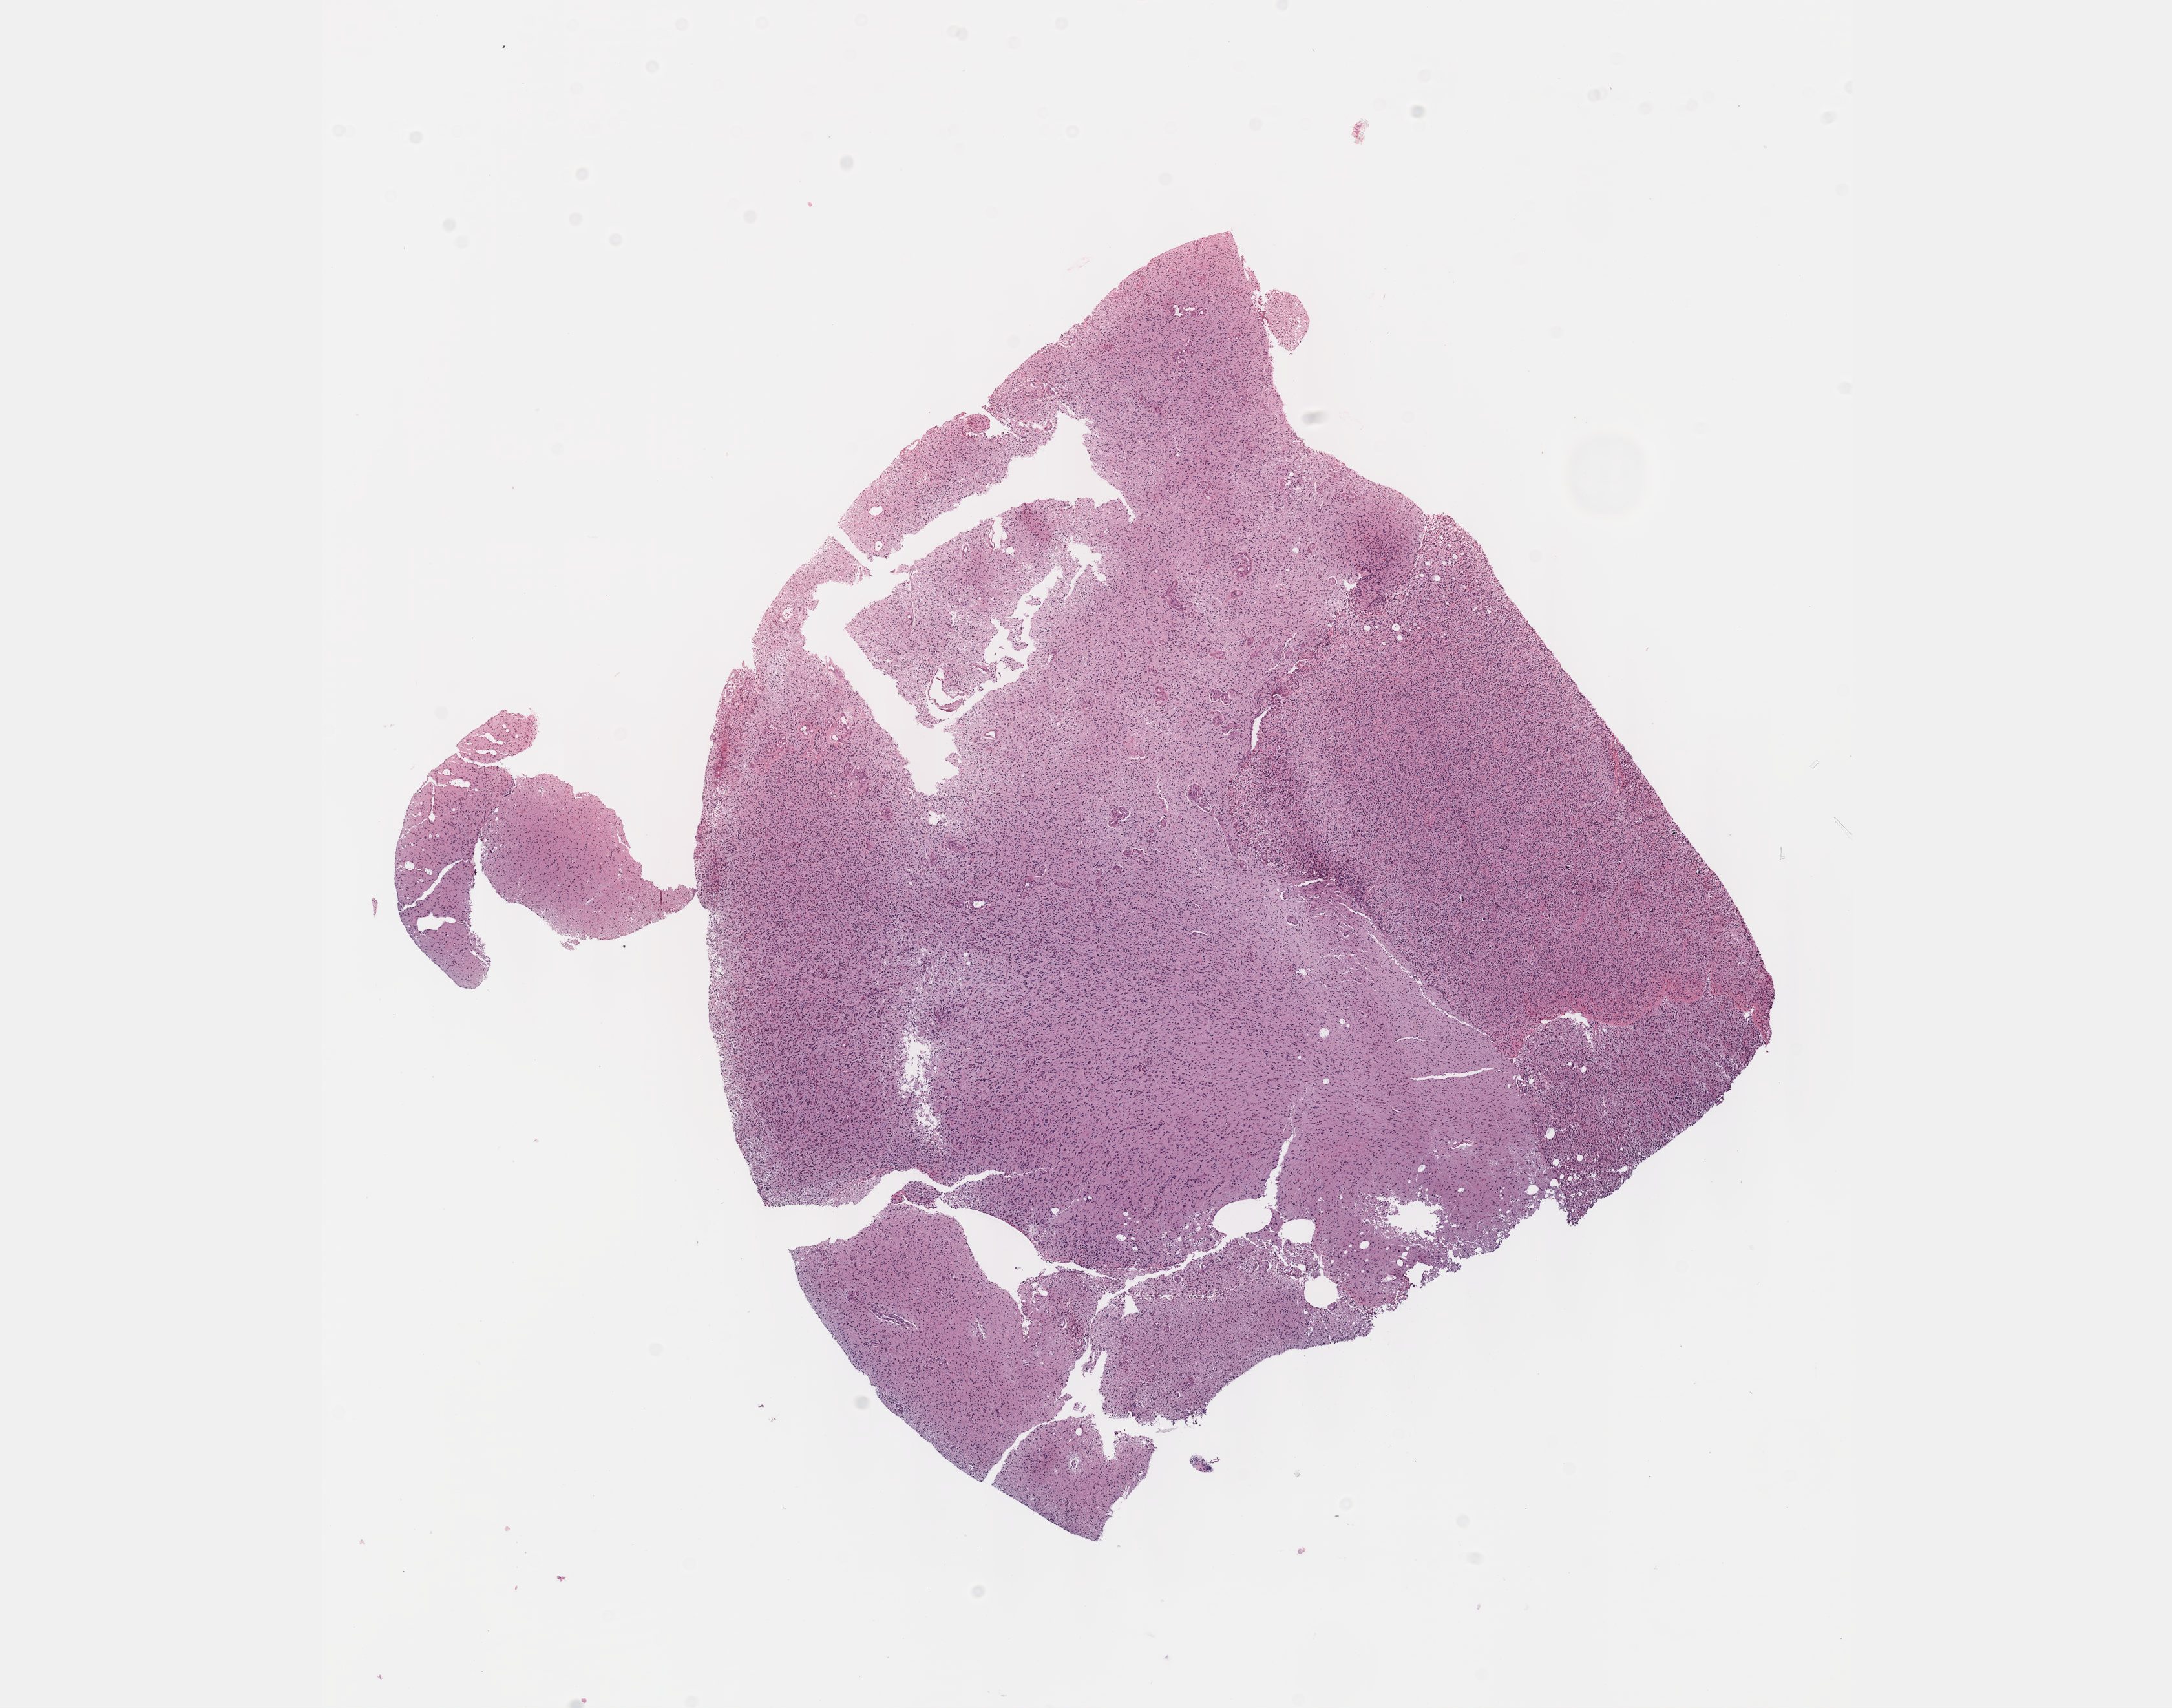
Digitized Hematoxylin and eosin (H&E) stained tissue section (whole slide) — shown as a low-resolution overview of the whole scanned area (about 13.6 x 10.7 mm); formalin-fixed paraffin-embedded (FFPE) diagnostic section; sample: primary tumour, brain. Male, age 59 years at initial diagnosis.
Histologic diagnosis: Astrocytoma, anaplastic (cerebrum).